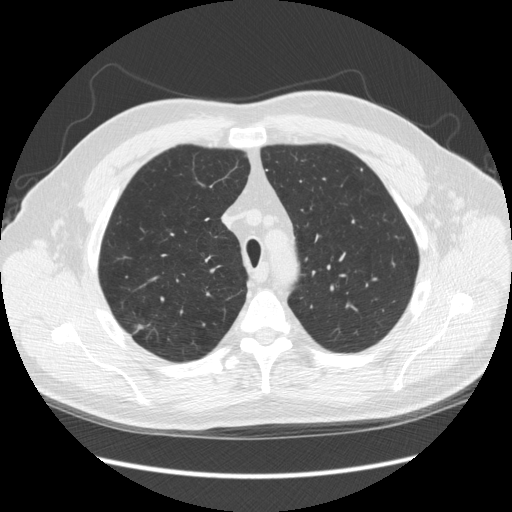
Axial slice from a low-dose chest CT screening exam. Third annual screen. Lung window (W 1500 / L -600 HU). 2.5 mm slice thickness. Standard (soft-tissue) reconstruction kernel (STANDARD). Male participant, aged 64 years at enrolment. Former smoker at enrolment.
Lesion marked by an expert reader, box from (x=118, y=312) to (x=168, y=354) px. The screening reader recorded 4 non-calcified nodules or masses ≥4 mm on this exam (right upper lobe, right upper lobe, right upper lobe, right upper lobe); which of them this box marks is not recorded. Lung cancer was diagnosed 15 days after this screen: adenocarcinoma, NOS, right upper lobe, moderately differentiated (G2), stage IA (AJCC 6th edition), 14 mm at pathology.